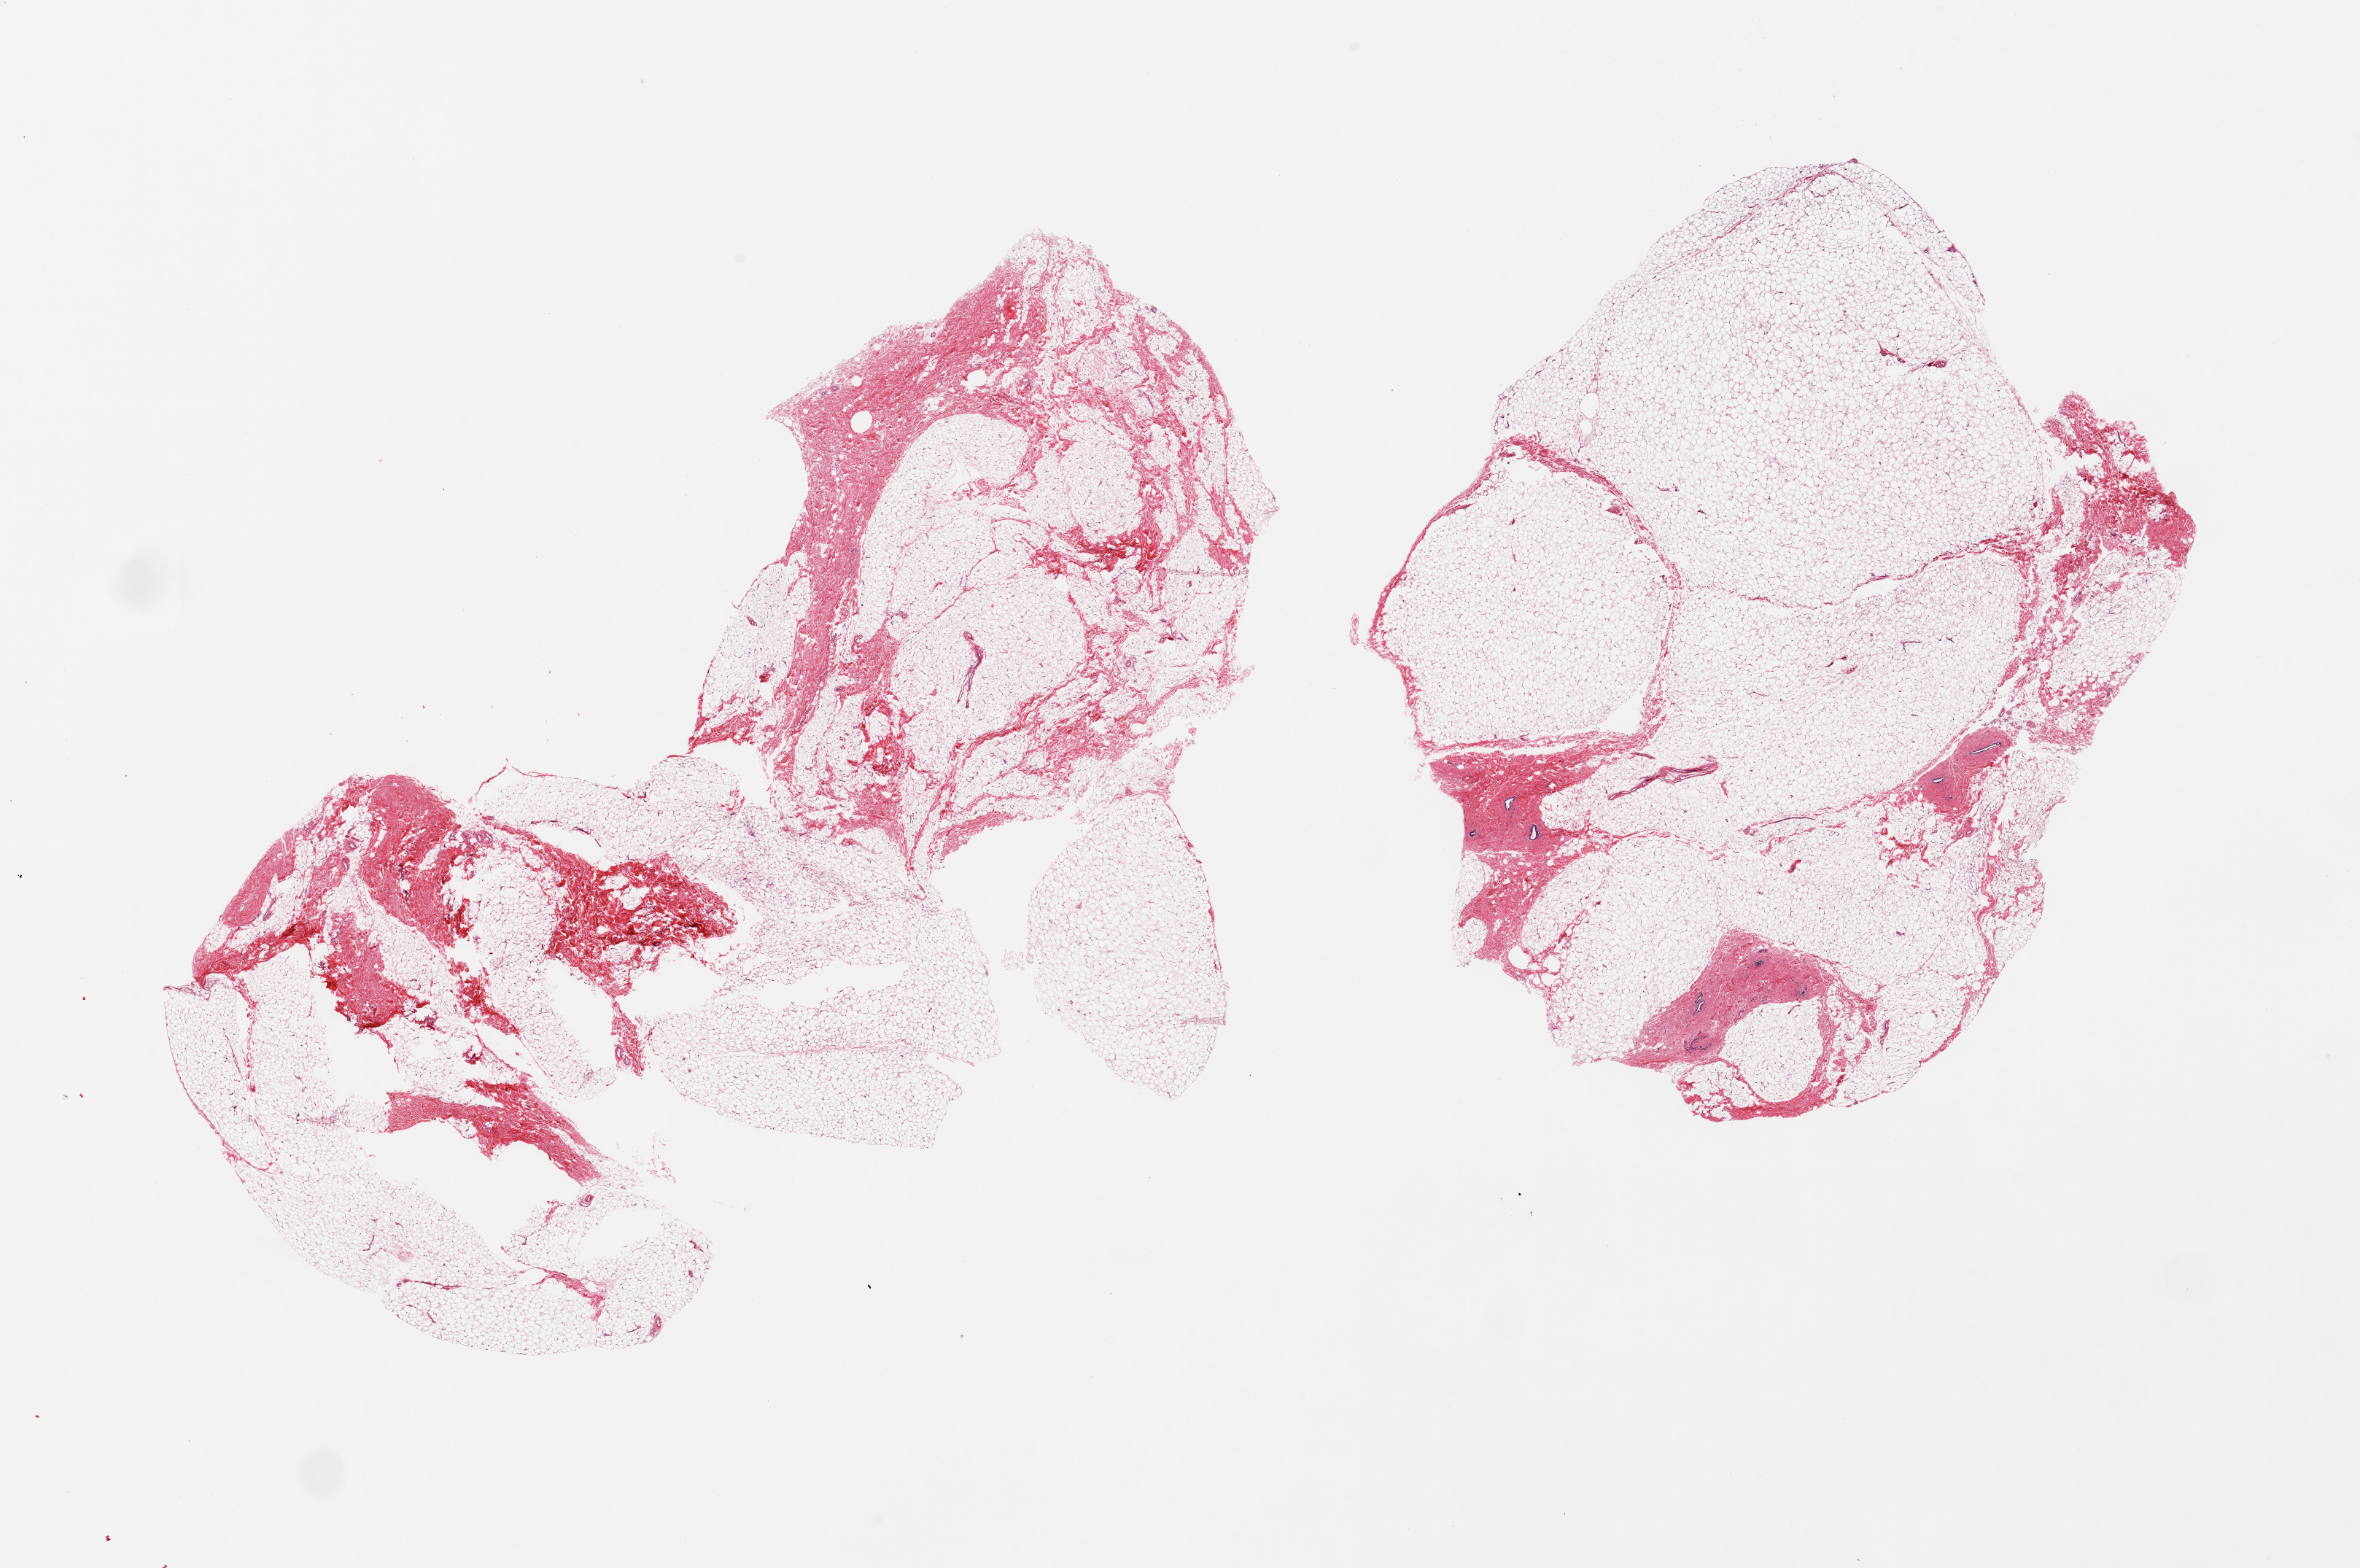
Haematoxylin and eosin whole-slide image, whole scanned area (about 25.6 x 17.0 mm, from a 20x scan) shown as a low-resolution overview, PAXgene-fixed, paraffin-embedded tissue, target tissue: breast, tissue donor sample. Donor: male.
Reviewer comment on this tissue sample: 2 pieces, fibroadipose elements, trace ducts.